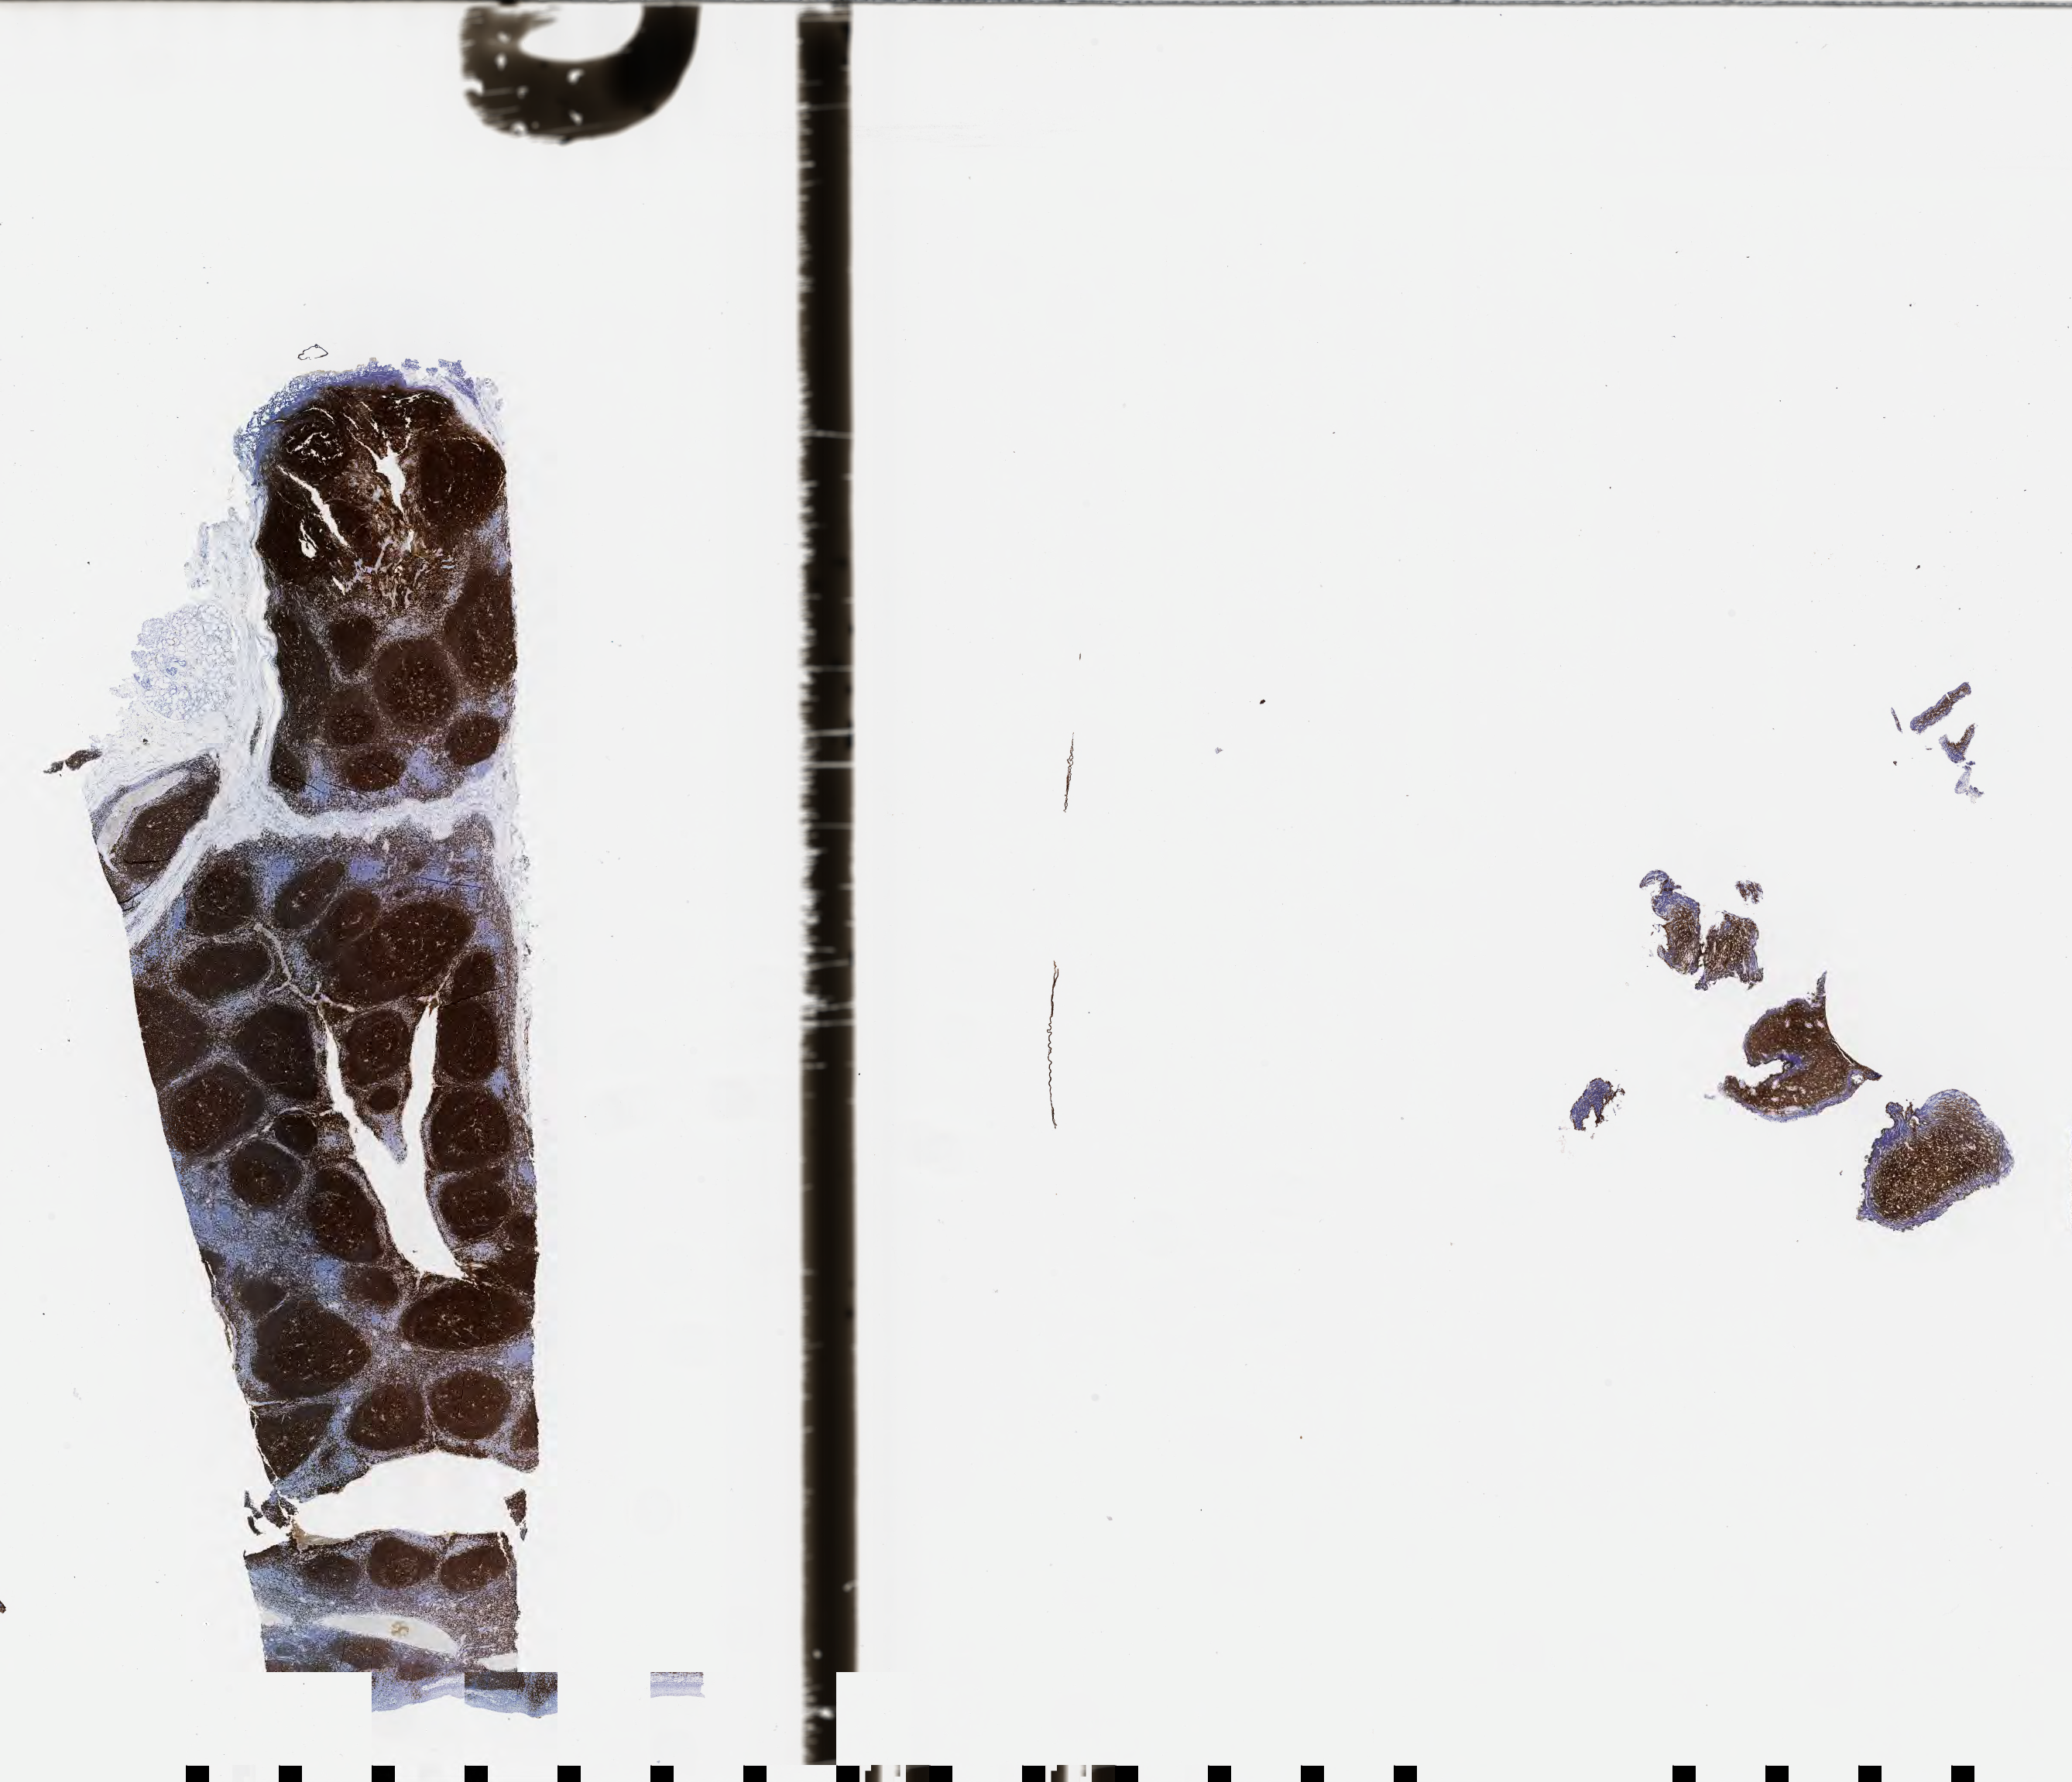
Whole-slide image, immunohistochemical stain for CD20, low-resolution overview of the scanned area, about 21.6 x 18.6 mm; specimen: tumor tissue; site: small intestine. Patient: female, 47 years old.
Diagnosis: Burkitt lymphoma, NOS.